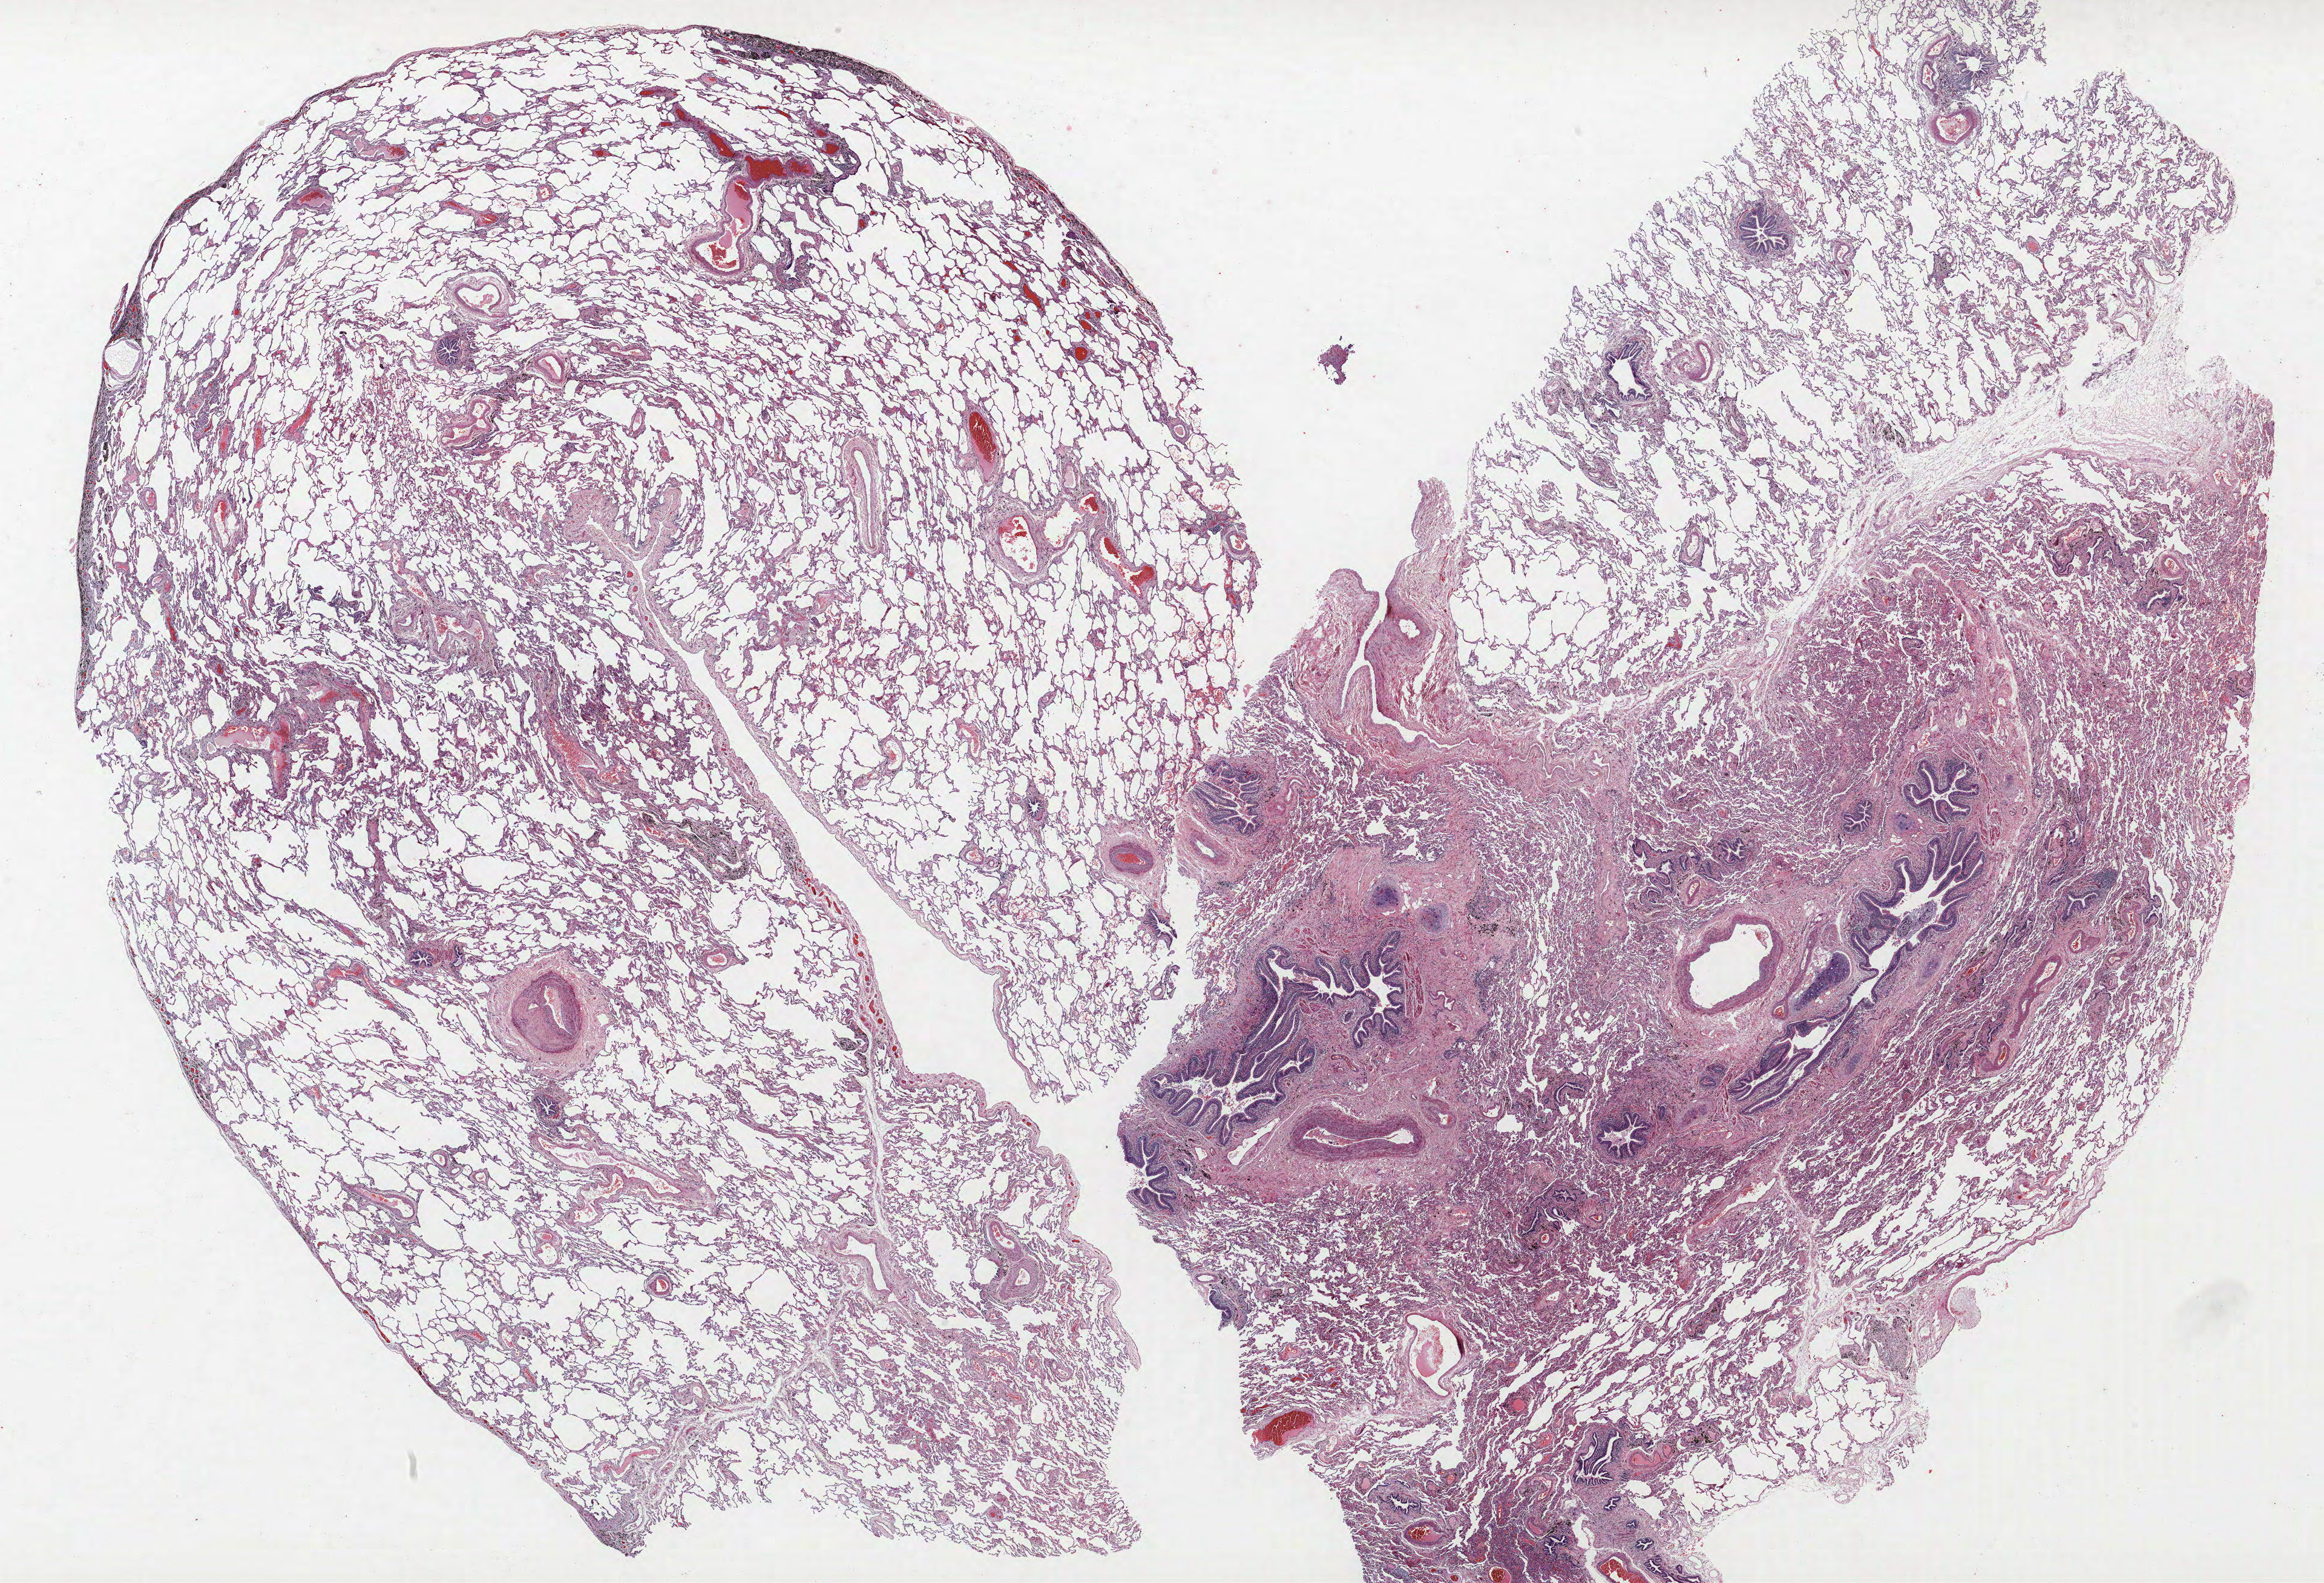
H&E whole-slide image — low-resolution overview of the scanned area, about 30.7 x 20.9 mm; formalin-fixed paraffin-embedded (FFPE) section; lung. Male, age 71 at enrolment. Former smoker at enrolment. Grade: moderately differentiated (G2).
• tumour size (pathology): 53 mm
• participant's lung-cancer diagnosis: Squamous cell carcinoma, NOS (ICD-O-3 8070/3)
• primary tumour location (clinical record): right lower lobe
• stage (AJCC 6th edition): IB